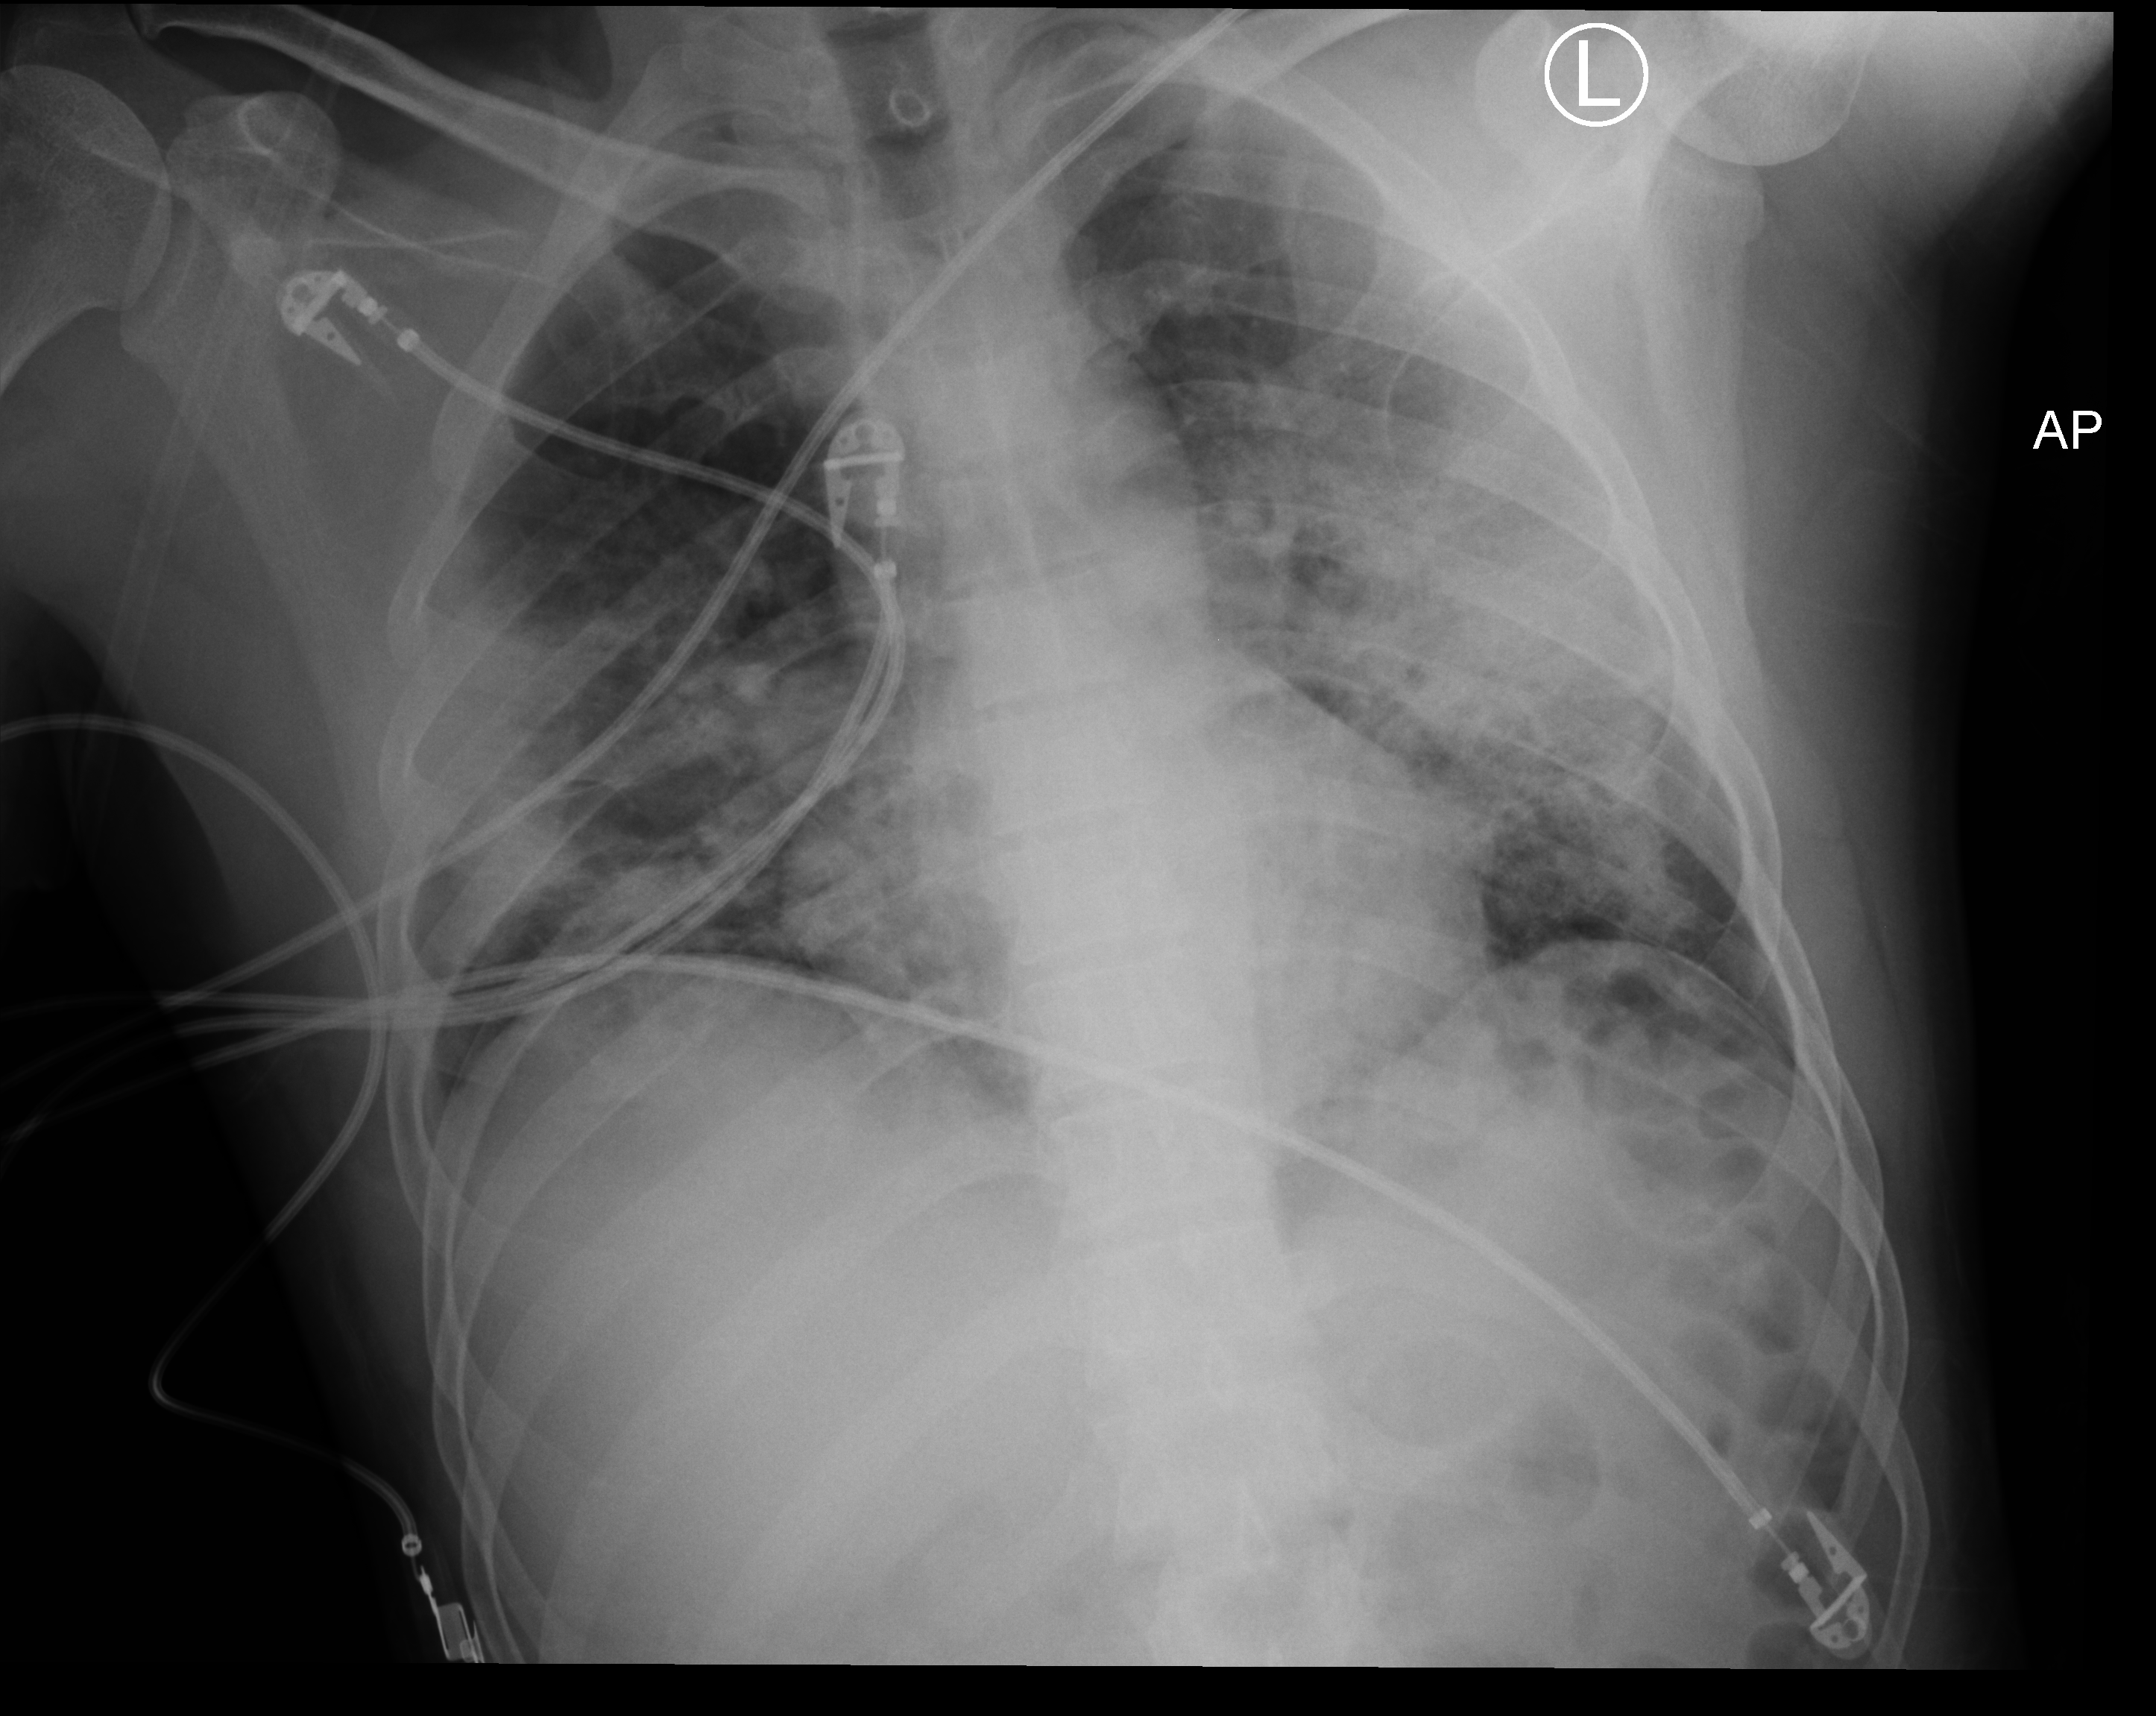
Portable chest radiograph; anteroposterior (AP) projection. Patient hospitalised with COVID-19; male, aged 18–59 years.
Hospital-stay facts (about this admission, not read from this image; timing relative to this image not recorded):
- other chronic lung disease (admission record): no
- admitted to intensive care during this hospital stay: yes
- smoking status (admission record): never